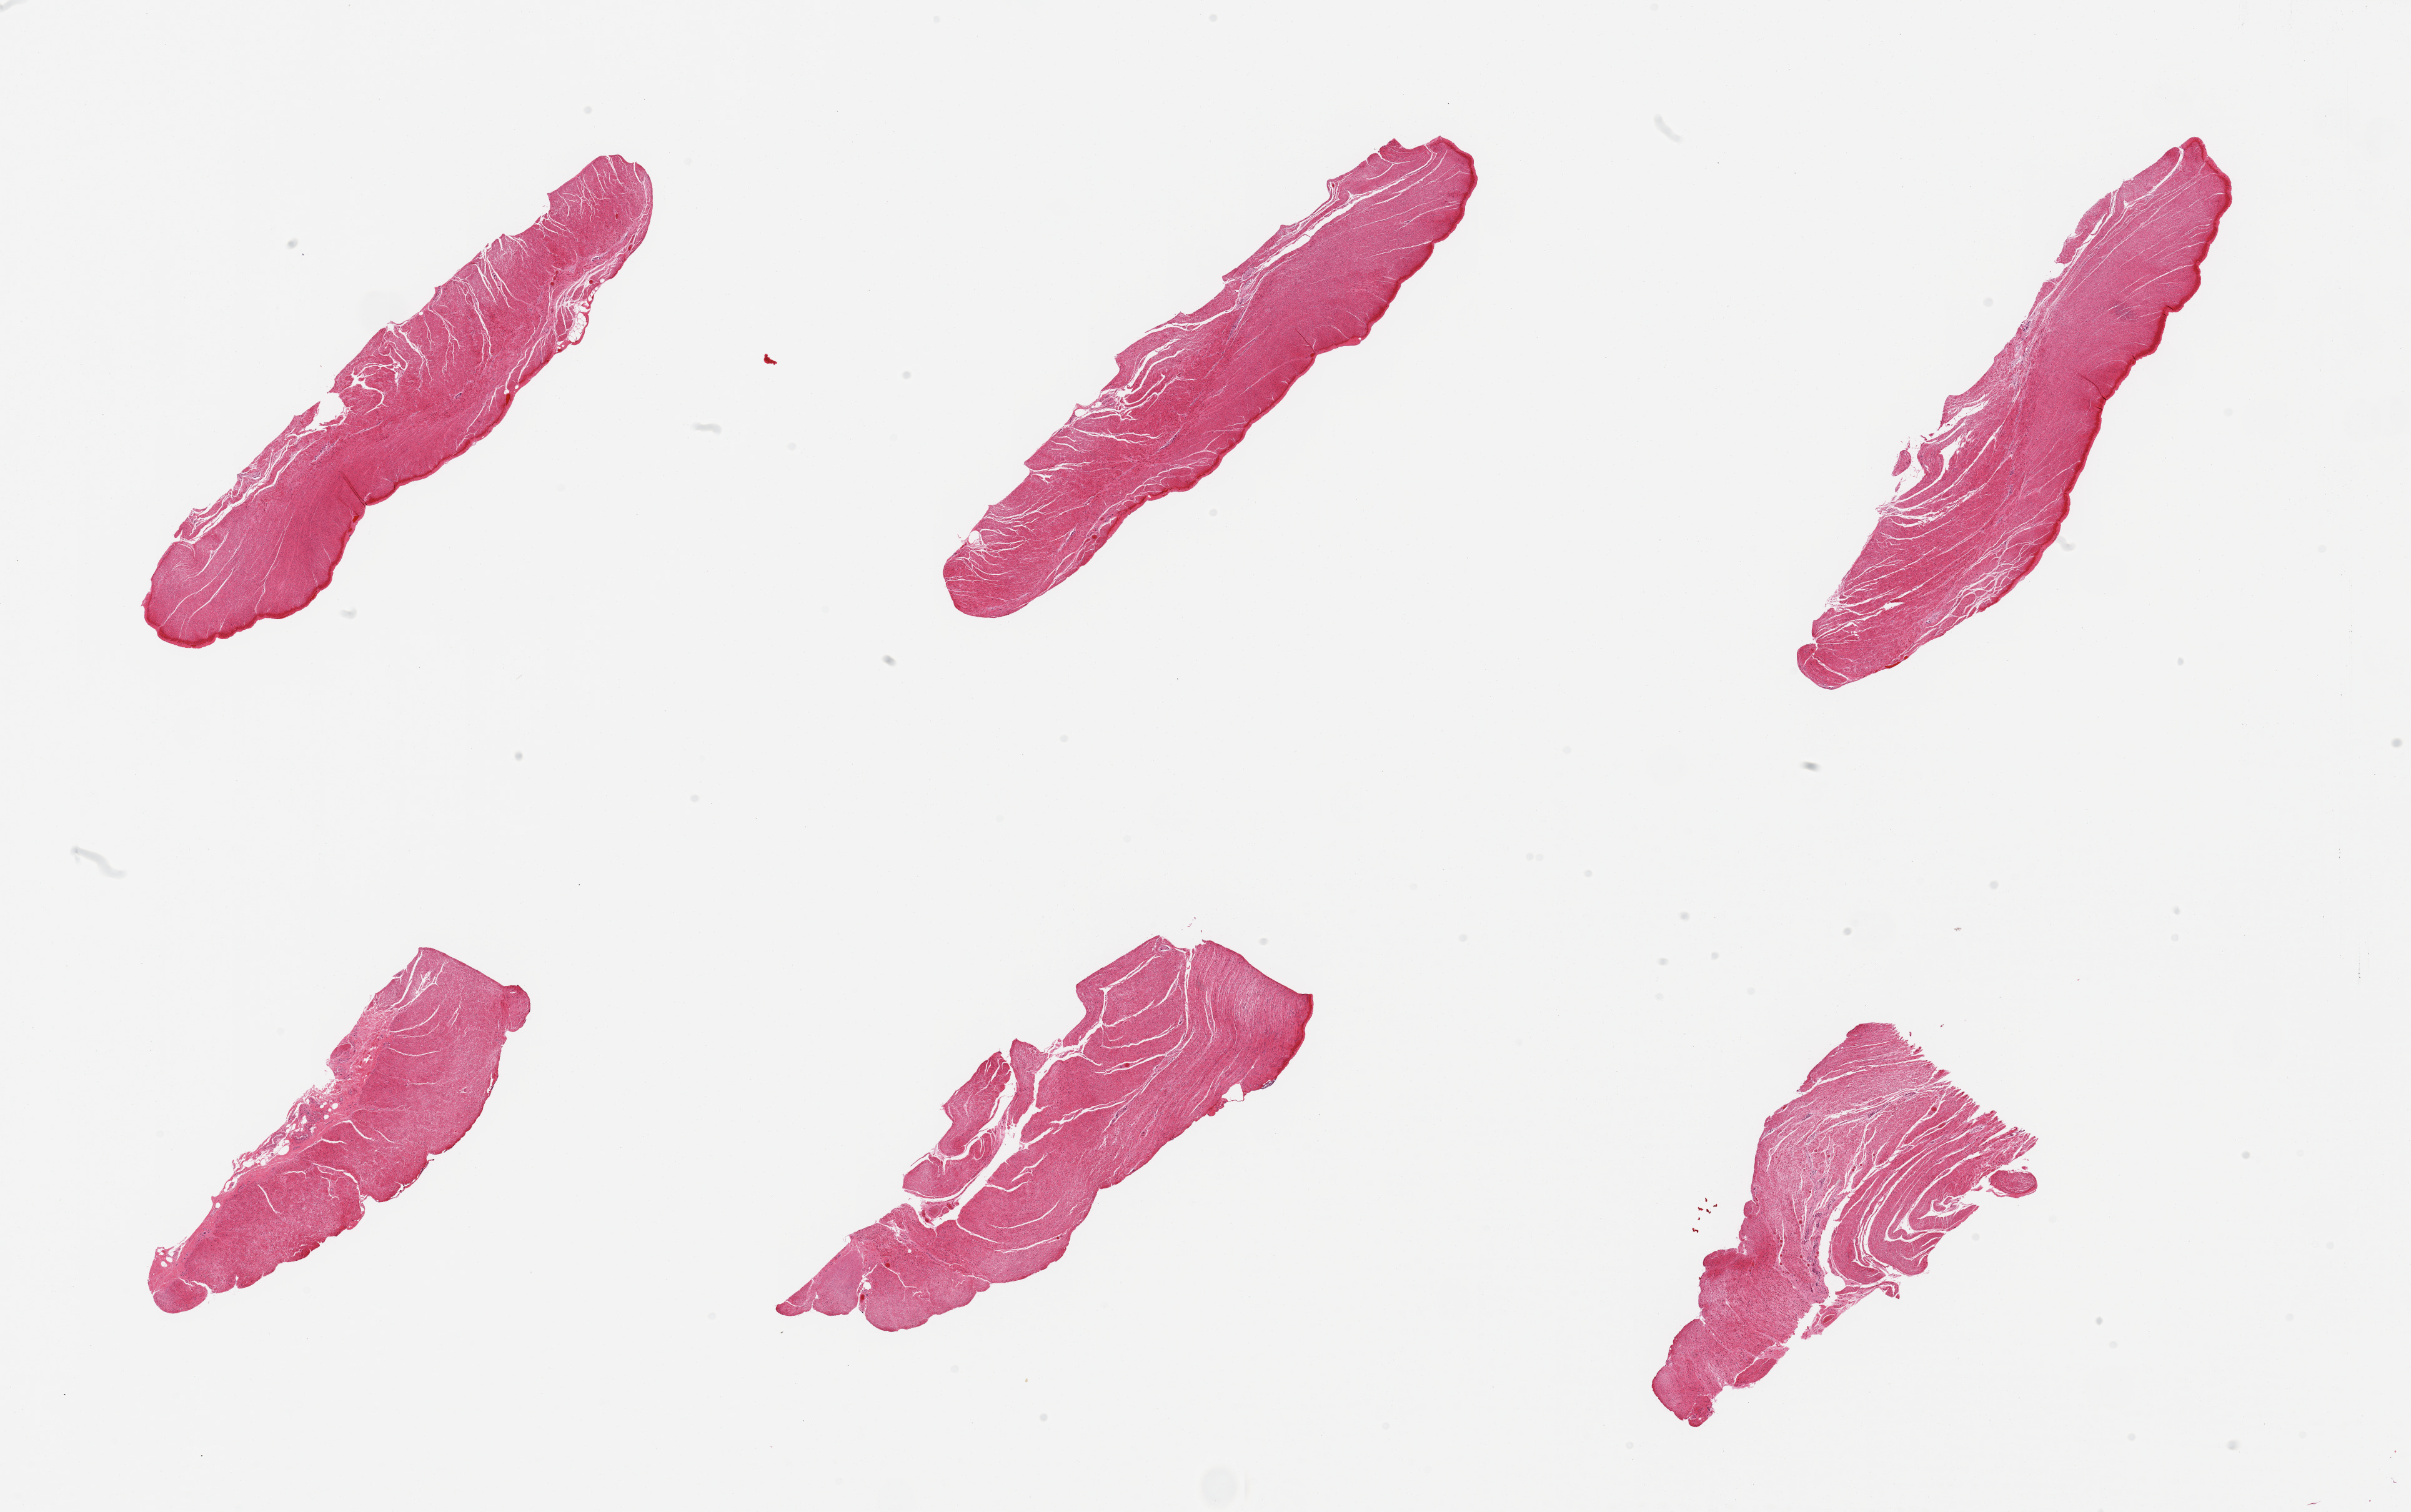
Whole-slide image, hematoxylin and eosin (H&E) stain, whole scanned area (about 30.5 x 19.1 mm) shown as a low-resolution overview; PAXgene-fixed, paraffin-embedded tissue; sampled site (target tissue): sigmoid colon; donor tissue sample. Donor sex: male.
Reviewer comment on this tissue sample: 6 pieces; well trimmed muscularis.